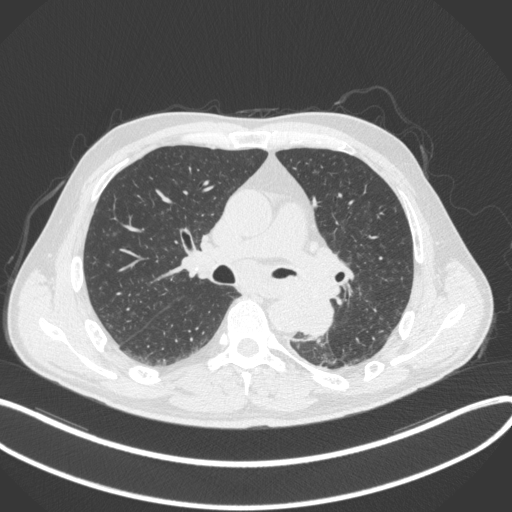
Chest CT, one axial slice. Position 203 of 328 along the scan axis. 120 kVp. Lung window (W 1500 / L -600 HU). 1 mm slice thickness. 512 × 512 image matrix, field of view 400 × 400 mm. Patient: male, 59 years. From the clinical record (not read from this slice): clinical TNM (as recorded): T2a N2 M0.
Annotated regions visible in this slice (bounding box drawn by a radiologist):
- lung tumour (recorded histology: squamous cell carcinoma): box from (x=294, y=288) to (x=336, y=338) px